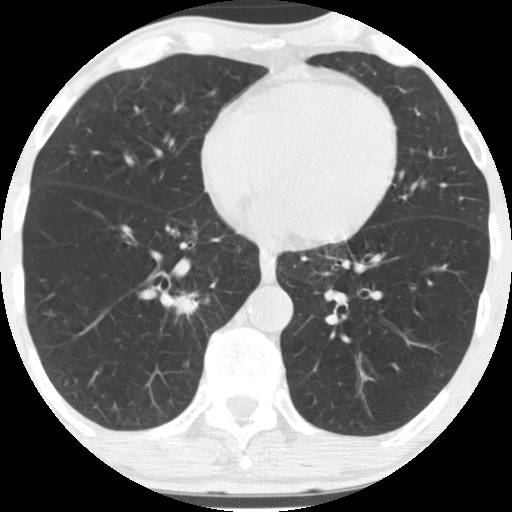
Low-dose screening chest CT, one axial slice. Position 59 of 170 along the scan axis. Lung window (W 1500 / L -600 HU). 2.5 mm slice thickness. 512 × 512 image matrix, field of view 290 × 290 mm.
Outlined on this slice (outlined manually by an expert reader):
- lesion 1 (tumor, lower lobe of right lung): bounding box <175,295,198,313> (left, top, right, bottom; pixels)